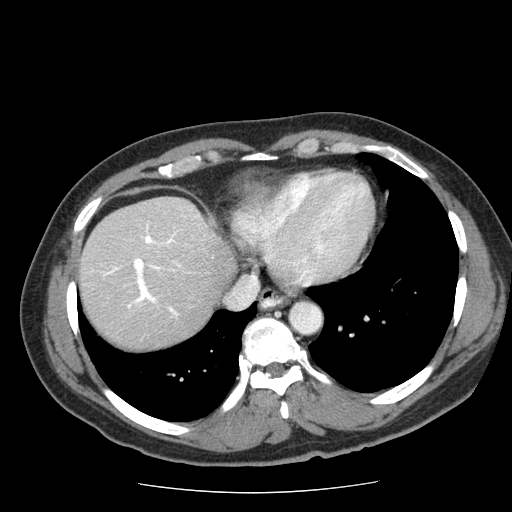
Contrast-enhanced abdominal CT (liver protocol), one axial slice; slice 61 of 85 in the series (ordered by position); soft-tissue window (W 400 / L 40 HU); 512 × 512 image matrix, field of view 360 × 360 mm. From the clinical record (not read from this slice): diagnosis: hepatocellular carcinoma (patient treated with transarterial chemoembolisation; whether this scan precedes or follows treatment is not stated here); TNM stage (as recorded): Stage-IIIA.
Structures marked on this image (semi-automatic segmentation, software-assisted and operator-edited):
- liver parenchyma outside the tumour (the mass and vessels are separate outlines, so this box may not span the whole liver): box from (x=78, y=196) to (x=236, y=348) px
- liver vessels: (x=103, y=225)–(x=181, y=316)